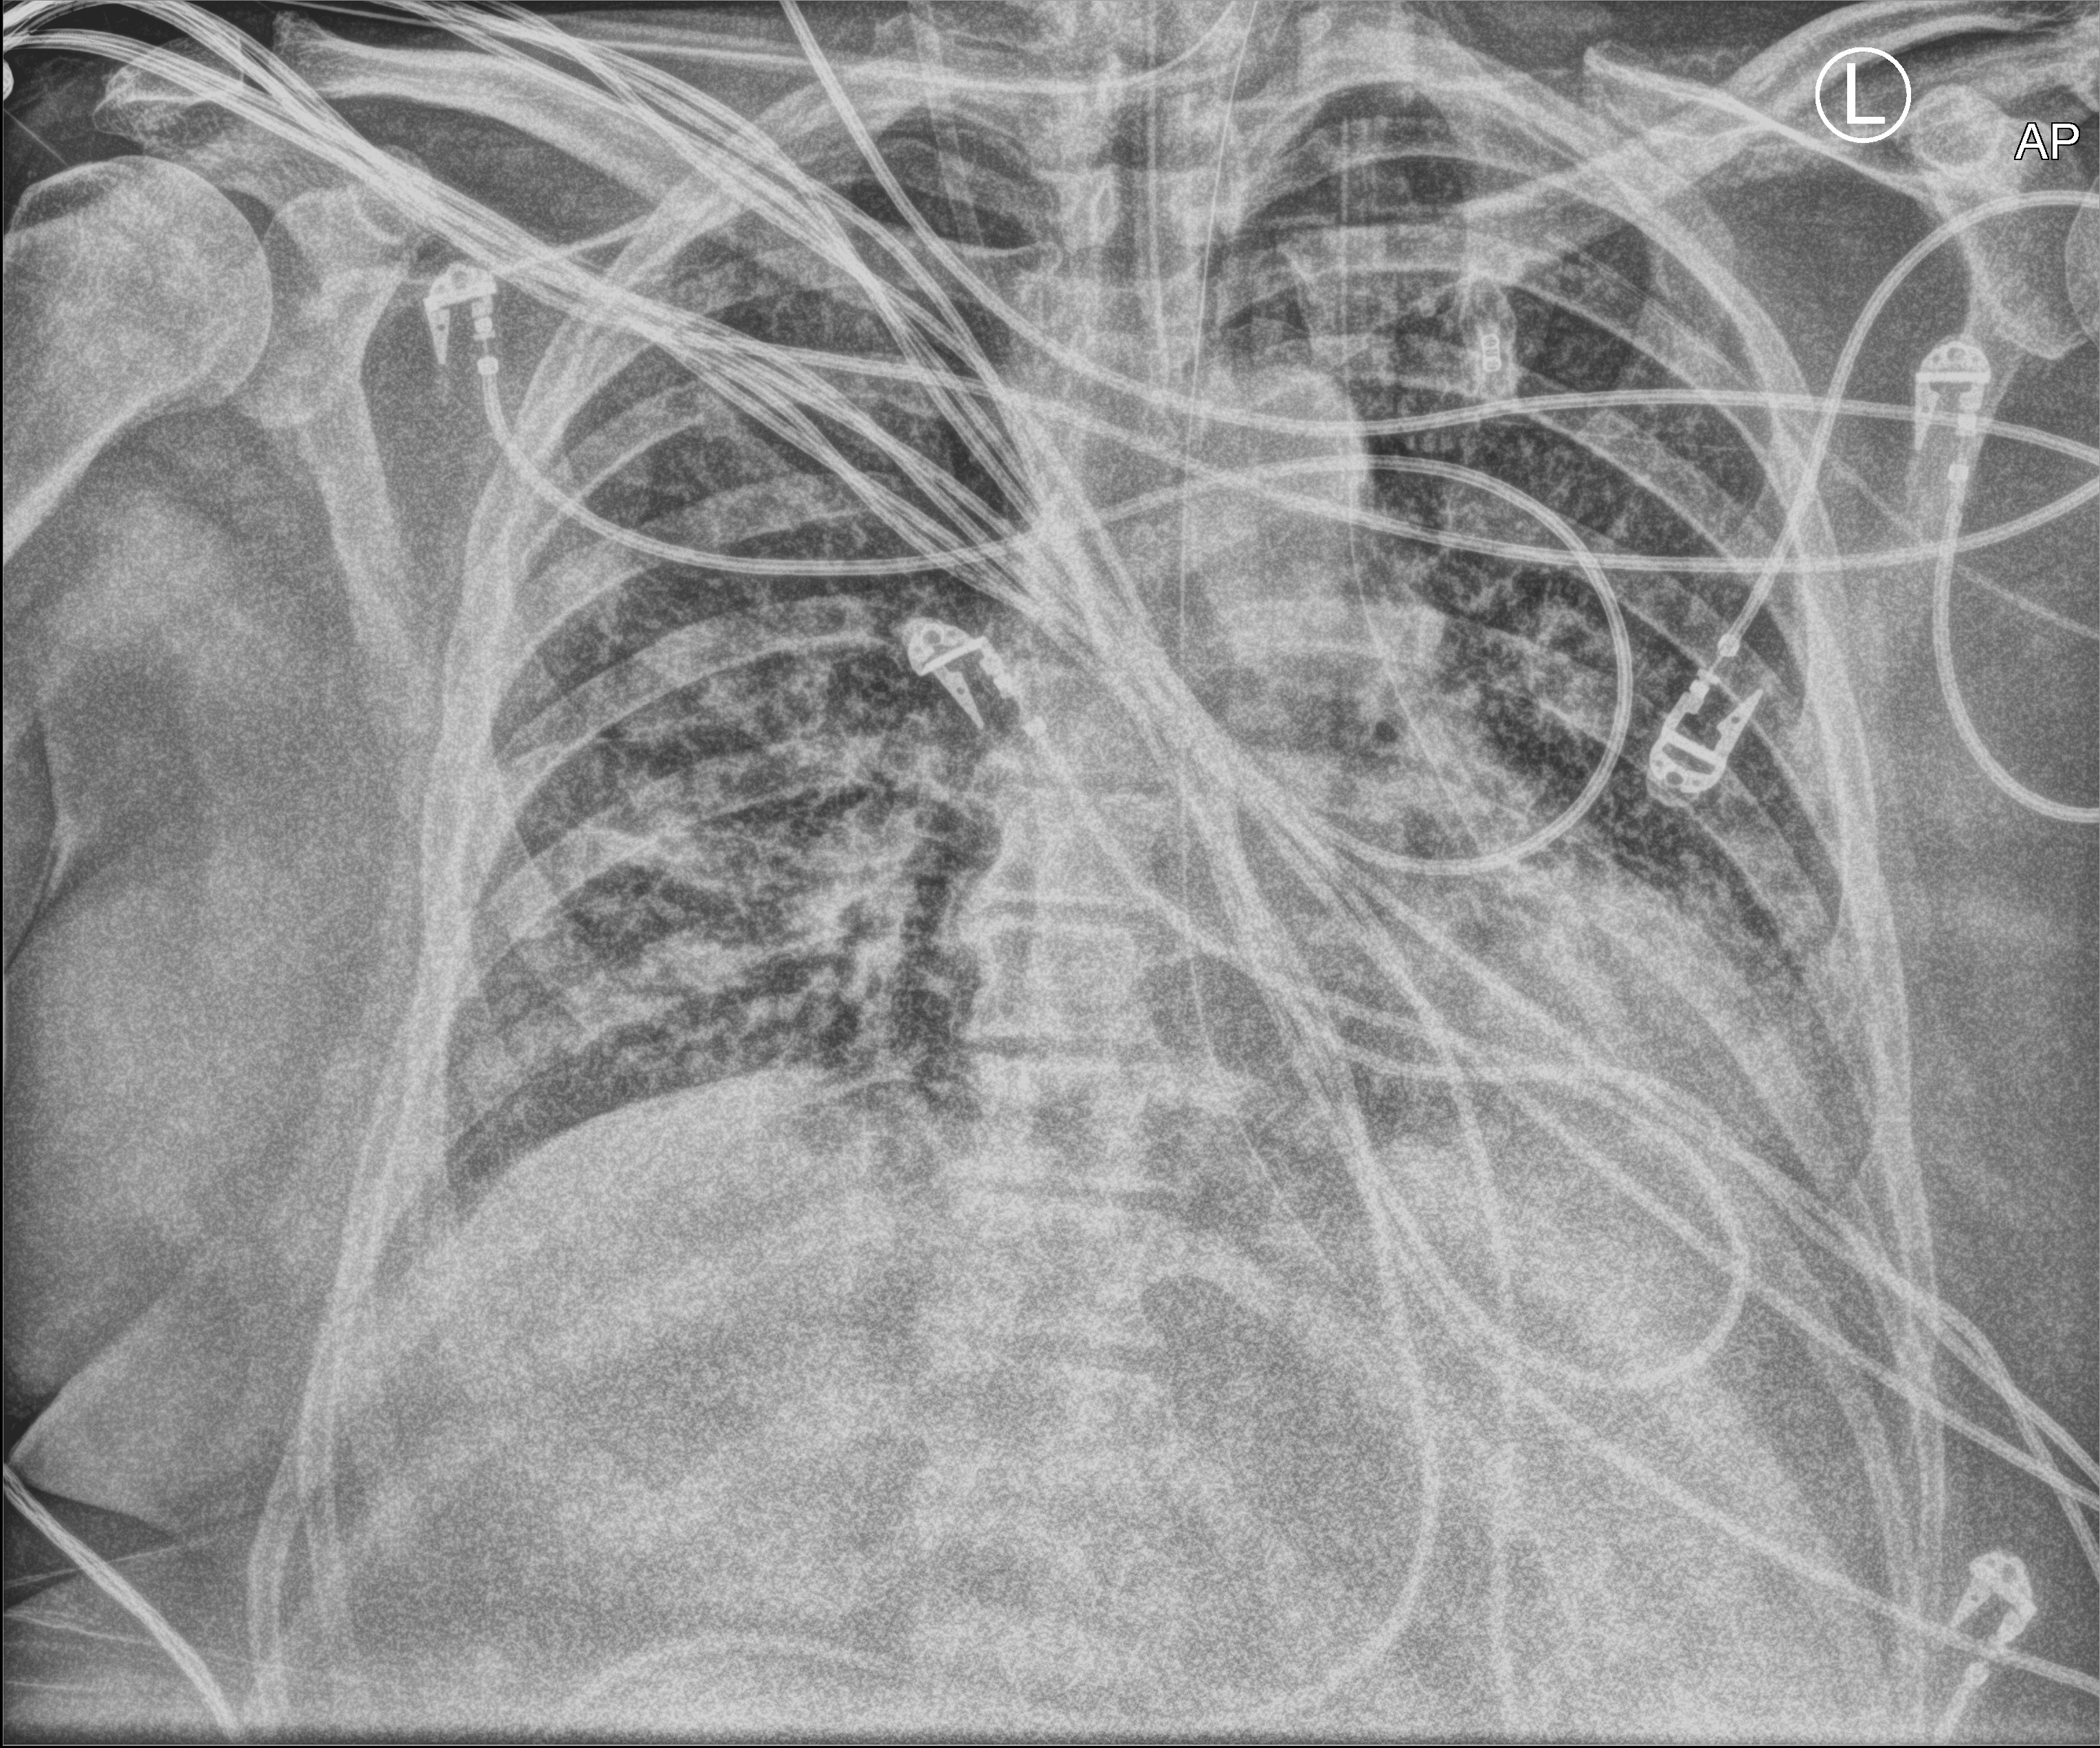
Bedside chest radiograph (computed radiography), anteroposterior (AP) projection. Patient hospitalised with COVID-19; male, aged 60–74 years.
From the hospital-stay record, not from the radiograph (when in the stay this image was taken is not recorded):
- diabetes (admission record): no
- hypertension (admission record): yes